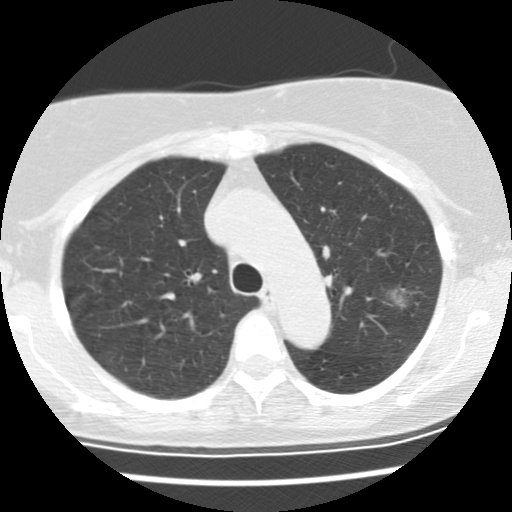
Low-dose screening chest CT, axial slice. Baseline screening round. Lung window (W 1500 / L -600 HU). Slice 102 of 137 in the series. Female, age 66 years at enrolment. Former smoker at enrolment.
Expert reader's lesion annotation, box from (x=375, y=278) to (x=428, y=325) px. The exam's reader record, not a measurement of the box and not confirmed to be the same lesion: non-calcified nodule or mass ≥4 mm, left upper lobe, 25 × 17 mm, poorly defined margins, mixed attenuation.